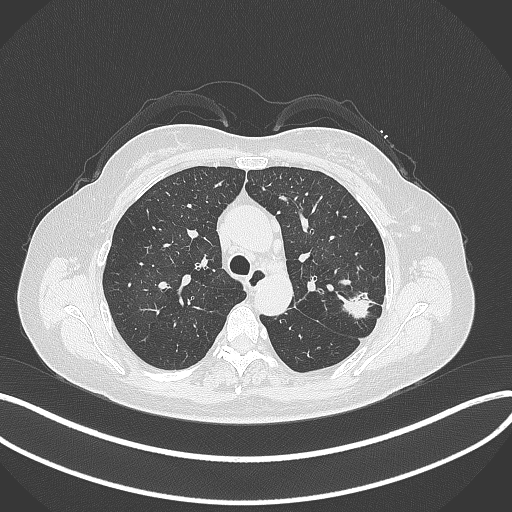
Chest CT, one axial slice; position 227 of 319 along the scan axis; reconstruction kernel B70f; lung window (W 1500 / L -600 HU); 1 mm slice thickness; 512 × 512 image matrix, field of view 400 × 400 mm. Female patient, age 60 years. From the clinical record (not read from this slice): clinical TNM (as recorded): T1c N0 M0.
Outlined on this slice (rectangle marked by the reading radiologist):
- lung tumour (recorded histology: adenocarcinoma): bounding box <336,286,375,319> (left, top, right, bottom; pixels)